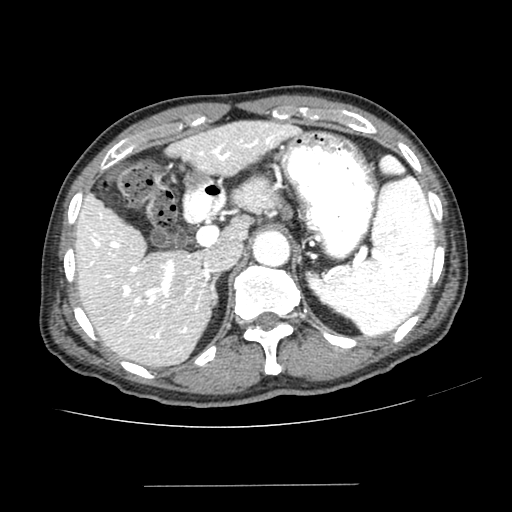
Contrast-enhanced abdominal CT (liver protocol), one axial slice; slice 156 of 187 in the series (ordered by position); one of 2 acquisitions stored at this slice position; soft-tissue window (W 400 / L 40 HU); 2.5 mm slice thickness; 512 × 512 image matrix, field of view 360 × 360 mm. Case-level facts recorded for this patient, not image findings: diagnosis: hepatocellular carcinoma (patient treated with transarterial chemoembolisation; whether this scan precedes or follows treatment is not stated here); TNM stage (as recorded): Stage-I; Child-Pugh class: A; tumour differentiation: poorly differentiated; tumour nodularity: uninodular.
Outlined on this slice (semi-automatic segmentation, software-assisted and operator-edited):
- liver parenchyma outside the tumour (the mass and vessels are separate outlines, so this box may not span the whole liver): box from (x=76, y=121) to (x=300, y=366) px
- liver vessels: (x=81, y=131)–(x=295, y=342)